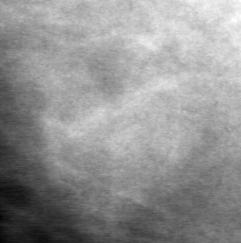
Crop from a digitized film mammogram around one marked abnormality, right breast, CC view, BI-RADS breast density category 2 (scale 1–4).
- Marked abnormality: mass, shape oval, margins obscured; BI-RADS assessment category 0; pathology result (as recorded, not read from the image): benign.